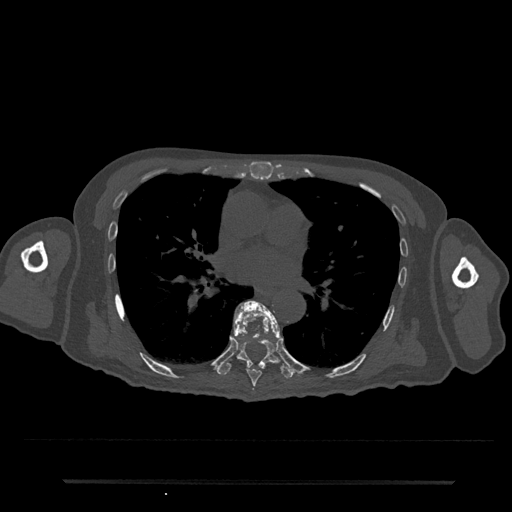
CT including the spine, one axial slice; bone window (W 1800 / L 400 HU); 512 × 512 image matrix. Patient: male, 74 years. From the clinical record (not read from this slice): primary cancer: prostate.
Structures marked on this image (semi-automatic segmentation, software-assisted and operator-edited):
- T7 vertebra: bounding box <233,301,280,387> (left, top, right, bottom; pixels)
- T8 vertebra: <216,301,294,379>